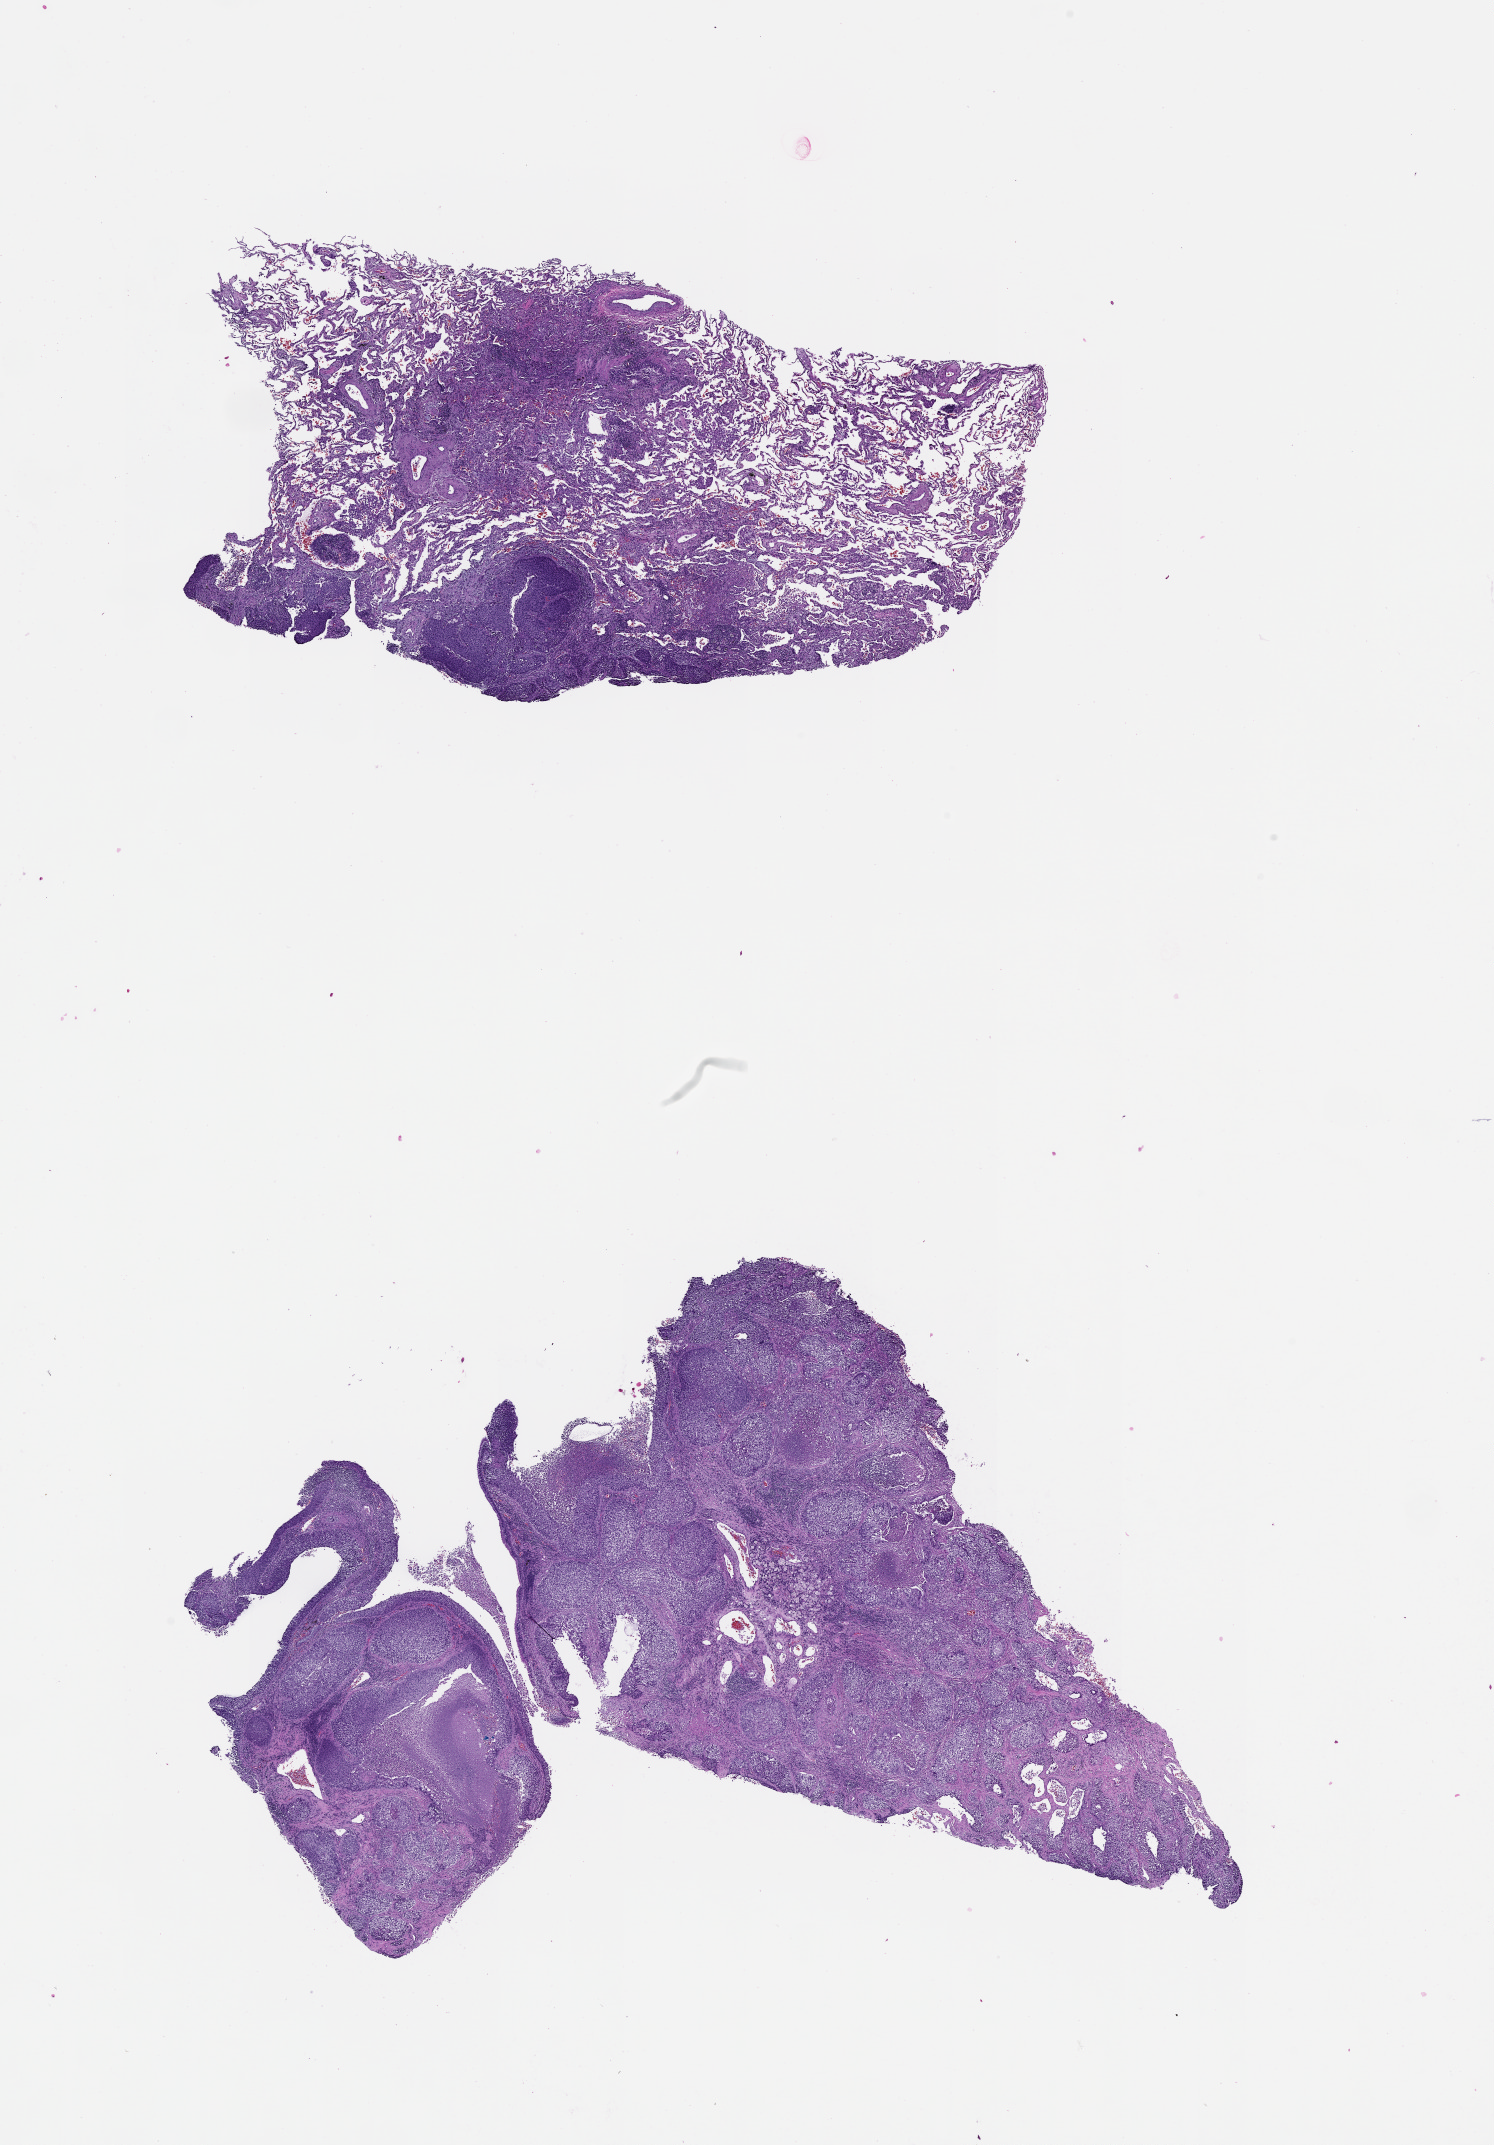
Digitized Hematoxylin and eosin (H&E) stained tissue section (whole slide), a low-resolution overview of the entire scanned area, about 12.0 x 17.3 mm, lung, tumour tissue. Patient: female, age 71 years.
Patient diagnosis (cohort enrolment): squamous cell carcinoma (lung).